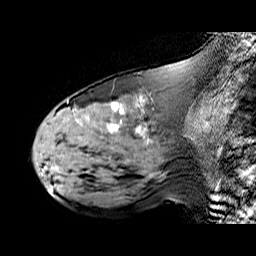
Breast MRI (dynamic contrast-enhanced), one sagittal slice; slice 27 of 60 in the series (ordered by position); dynamic contrast-enhanced series, time point 2 of 6 at this slice position (early post-contrast); 1.5 T; TE 6.3 ms, TR 32.9 ms; 256 × 256 image matrix. Female patient. Case-level facts recorded for this patient, not image findings: setting: breast cancer imaged before/during neoadjuvant chemotherapy; receptor status: HER2-positive.
Structures marked on this image (semi-automatic segmentation, software-assisted and operator-edited):
- analysis volume of interest (the breast-tissue region the enhancement analysis was run in; not a lesion): bounding box <48,92,195,174> (left, top, right, bottom; pixels)
- tumour enhancement mask (voxels above the 100 % enhancement threshold inside the analysis volume of interest): <107,103,124,131>